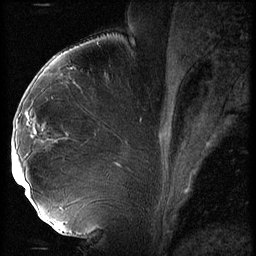
Breast MRI (dynamic contrast-enhanced), one sagittal slice; slice 33 of 56 in the series (ordered by position); 3 images stored at this slice position (order not interpretable as contrast timing); 1.5 T; TE 4.2 ms, TR 9 ms; 2.5 mm slice thickness; 256 × 256 image matrix. Female patient, age 43 years. From the clinical record (not read from this slice): setting: breast cancer imaged before/during neoadjuvant chemotherapy; receptor status: HER2-positive.
Annotated regions visible in this slice (semi-automatically segmented with operator editing):
- analysis volume of interest (the breast-tissue region the enhancement analysis was run in; not a lesion): bounding box (x1, y1, x2, y2) in pixels: (13, 92, 74, 211)
- tumour enhancement mask (voxels above the 140 % enhancement threshold inside the analysis volume of interest): (13, 145, 30, 199)